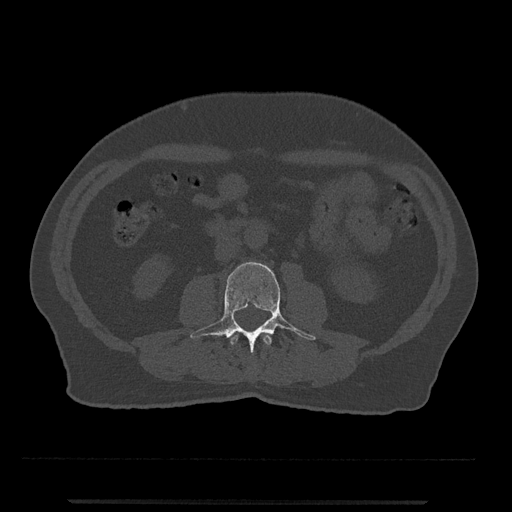
CT including the spine, one axial slice; position 206 of 797 along the scan axis; 120 kVp; bone window (W 1800 / L 400 HU); 0.5 mm slice thickness; 512 × 512 image matrix, field of view 419 × 419 mm. Patient: male, 63 years. From the clinical record (not read from this slice): primary cancer: prostate.
Structures marked on this image (semi-automatic segmentation, software-assisted and operator-edited):
- L2 vertebra: bounding box [x1, y1, x2, y2] px = [230, 333, 272, 346]
- L3 vertebra: [190, 262, 316, 354]